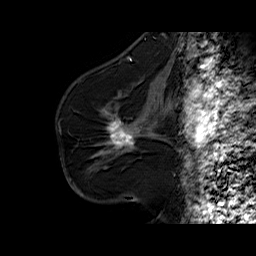
Breast MRI (dynamic contrast-enhanced), one sagittal slice; dynamic contrast-enhanced series, time point 2 of 6 at this slice position (early post-contrast); 1.5 T; TE 6.3 ms, TR 32.5 ms; 4 mm slice thickness; 256 × 256 image matrix, field of view 200 × 200 mm. Female patient. From the clinical record (not read from this slice): setting: breast cancer imaged before/during neoadjuvant chemotherapy; receptor status: HR-positive, HER2-negative.
Annotated regions visible in this slice (semi-automatically segmented with operator editing):
- analysis volume of interest (the breast-tissue region the enhancement analysis was run in; not a lesion): bounding box <94,103,161,164> (left, top, right, bottom; pixels)
- tumour enhancement mask (voxels above the 100 % enhancement threshold inside the analysis volume of interest): <107,118,134,148>